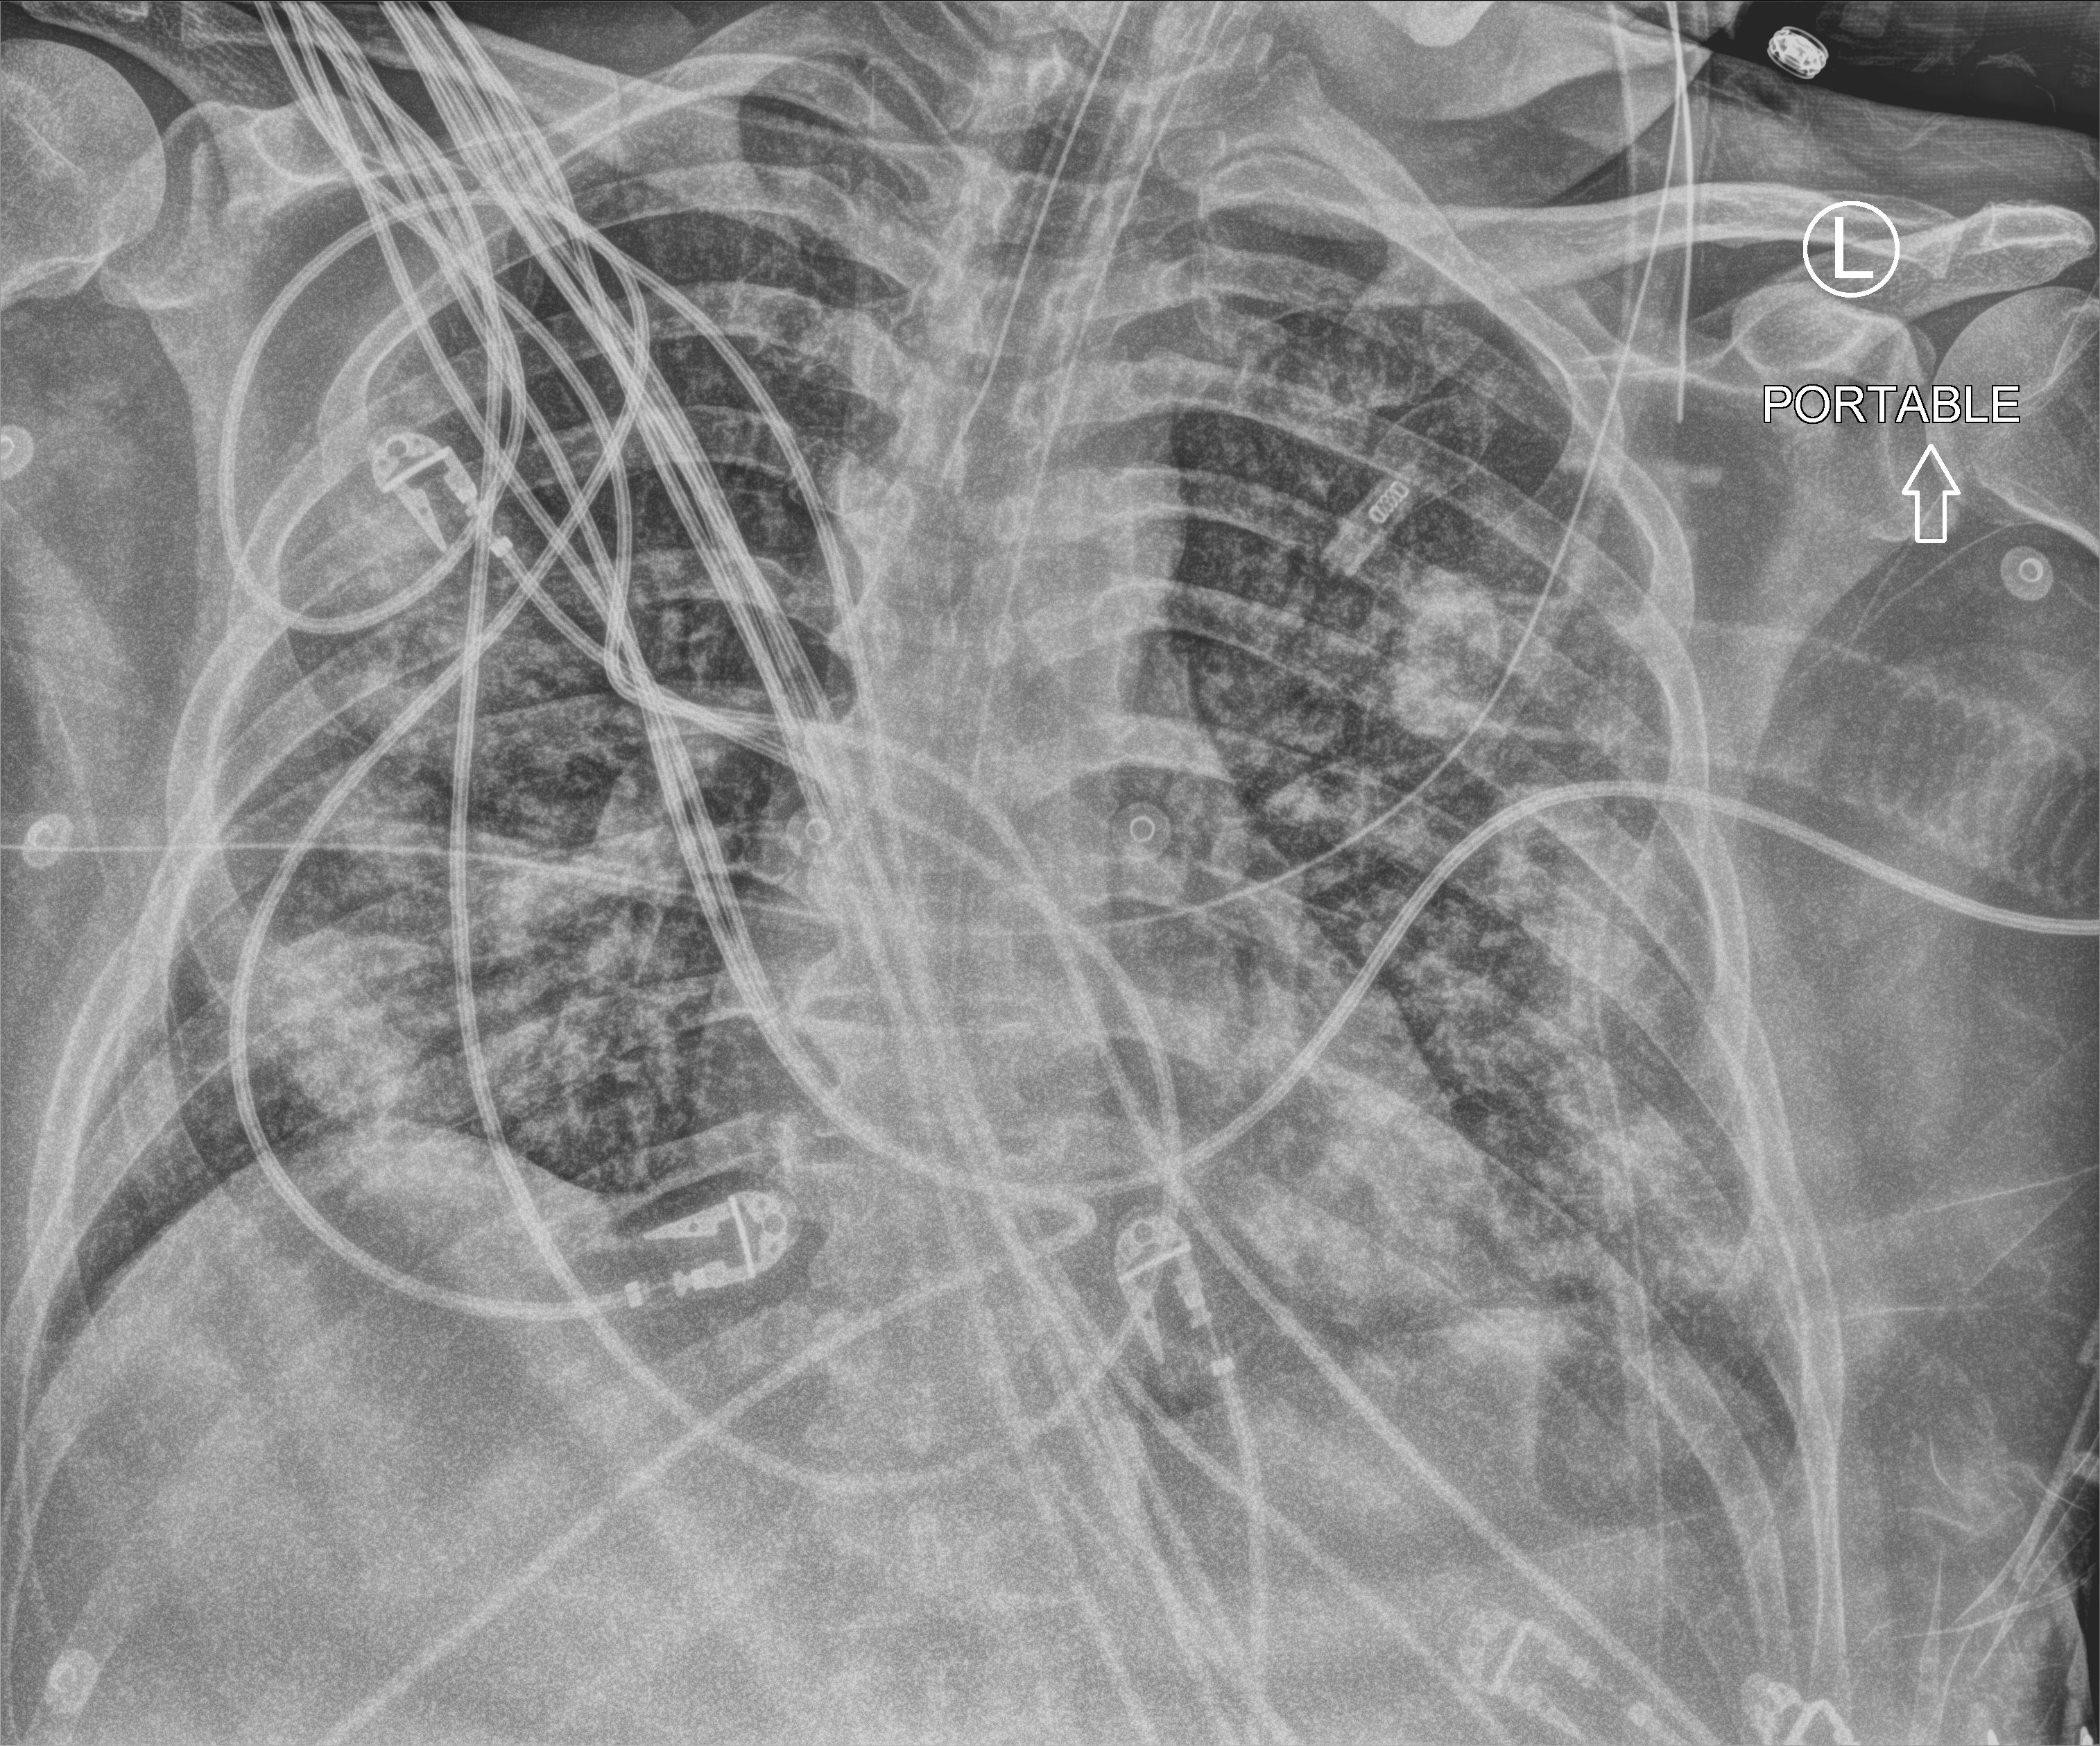
Bedside chest radiograph (computed radiography); anteroposterior (AP) projection. Patient hospitalised with COVID-19; male, aged 18–59 years.
Hospital-stay facts (about this admission, not read from this image; timing relative to this image not recorded):
- mechanically ventilated during this hospital stay: yes
- admitted to intensive care during this hospital stay: yes